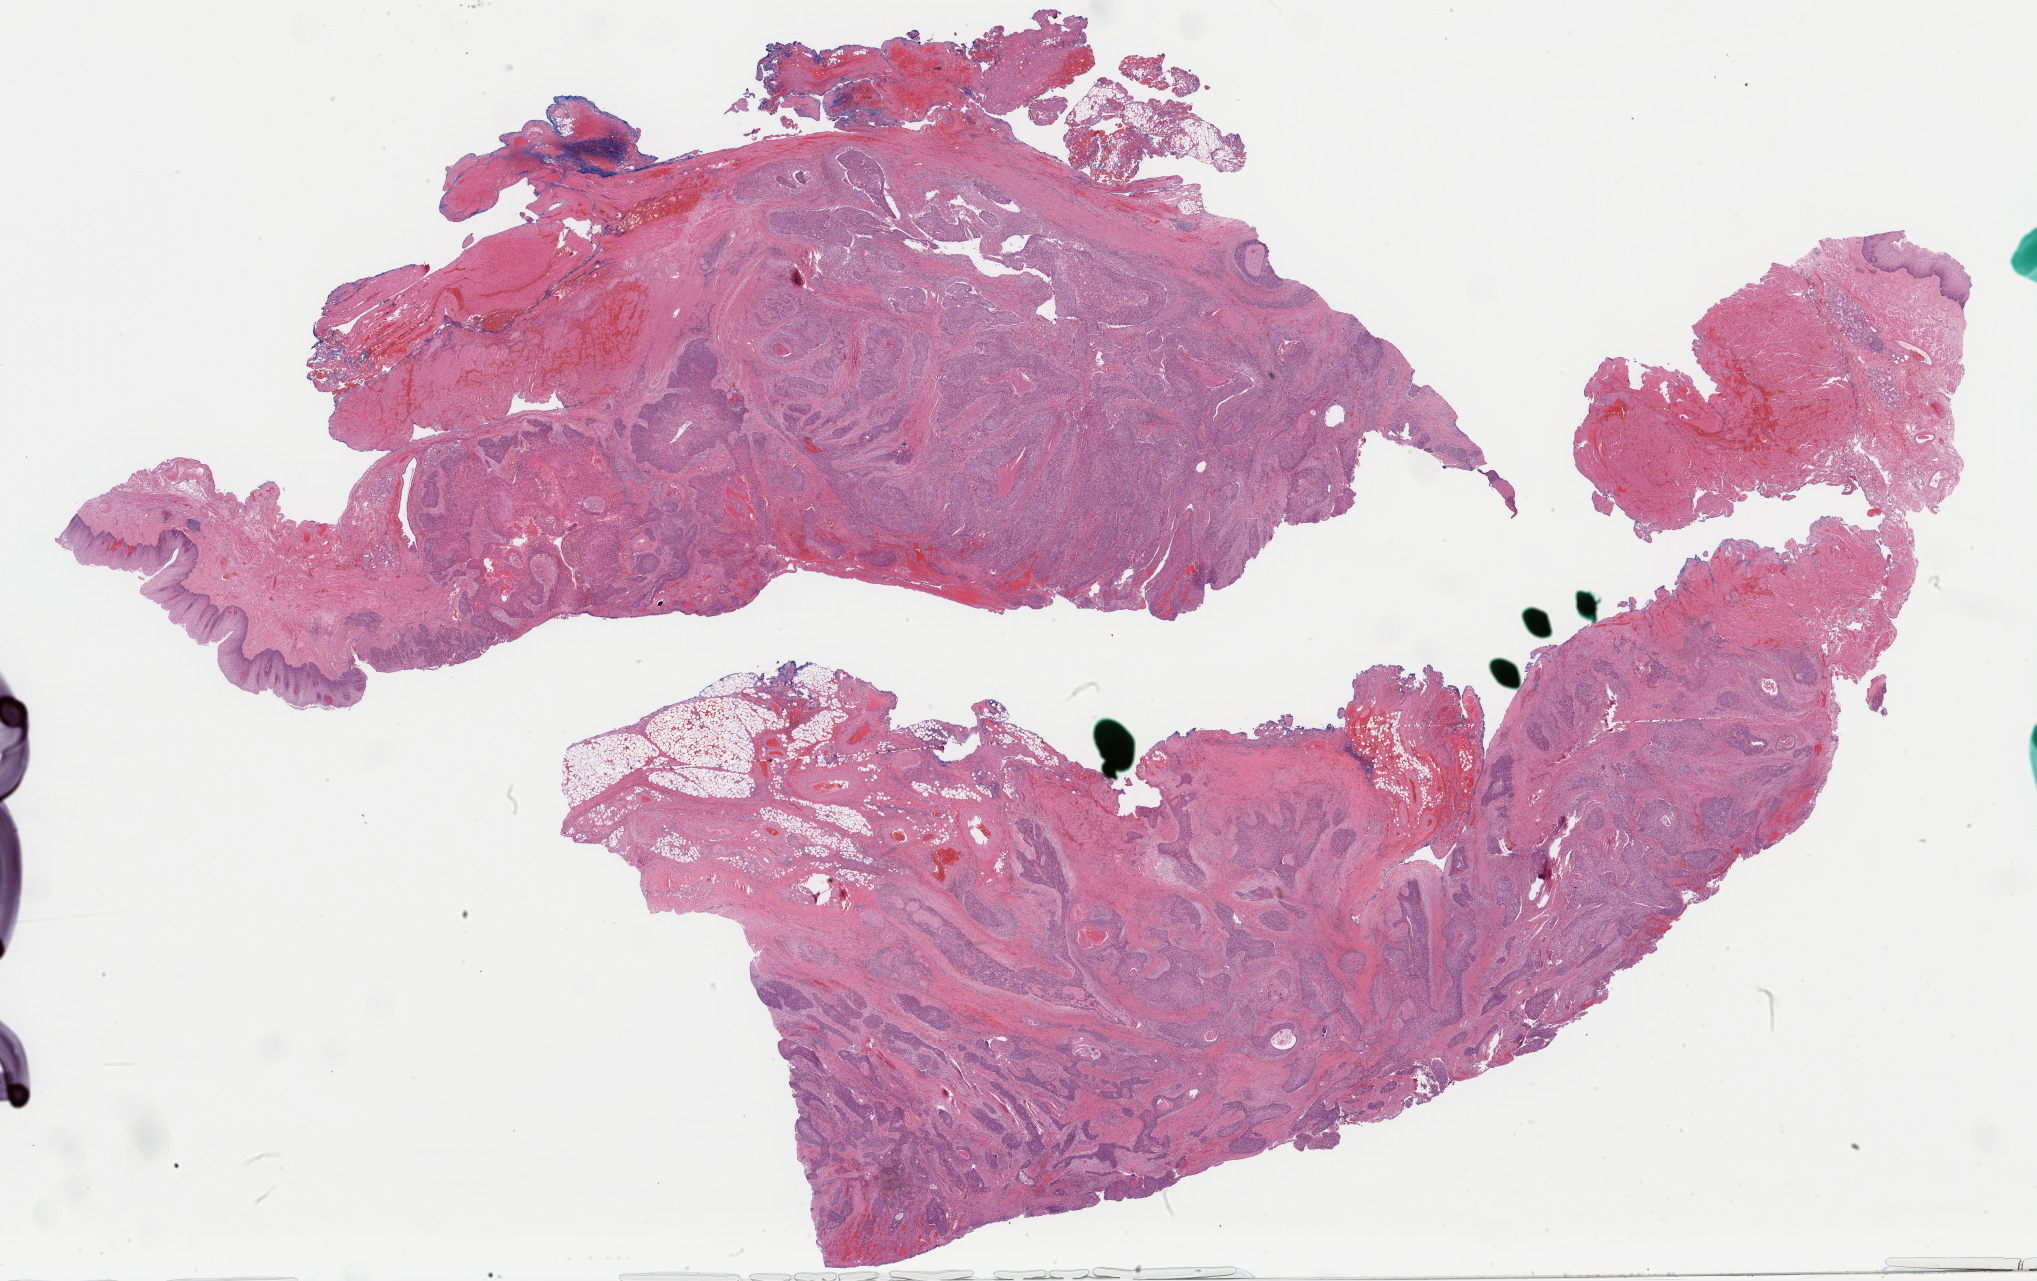
Hematoxylin and eosin (H&E) stained whole-slide image — a low-resolution overview of the entire scanned area, about 32.2 x 20.2 mm (slide scanned at 40x); formalin-fixed paraffin-embedded (FFPE) diagnostic section; esophagus, primary tumour sample. Patient: male, age at initial diagnosis 75 years.
Histologic diagnosis: Squamous cell carcinoma, NOS (middle third of esophagus).